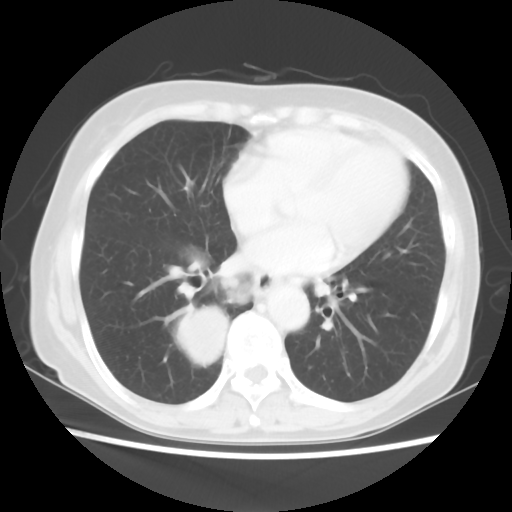
Chest CT, one axial slice; position 22 of 56 along the scan axis; reconstruction kernel STANDARD; lung window (W 1500 / L -600 HU); 5 mm slice thickness; 512 × 512 image matrix, field of view 332 × 332 mm. Female patient, age 66 years. Case-level facts recorded for this patient, not image findings: clinical TNM (as recorded): T2 N3 M0; histopathological grade: G3.
Structures marked on this image (bounding box drawn by a radiologist):
- lung tumour (recorded histology: small cell carcinoma): bounding box <178,303,231,373> (left, top, right, bottom; pixels)